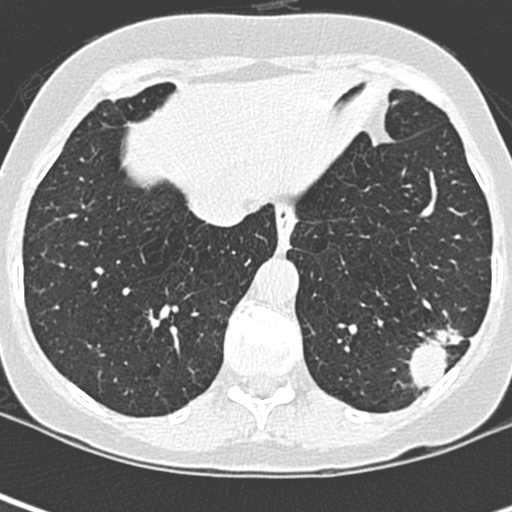
Low-dose screening chest CT, one axial slice; slice 73 of 252 in the series (ordered by position); lung window (W 1500 / L -600 HU); 1.3 mm slice thickness; 512 × 512 image matrix.
Structures marked on this image (manually delineated by an expert):
- lesion 1 (tumor, lower lobe of left lung): box from (x=405, y=324) to (x=464, y=390) px